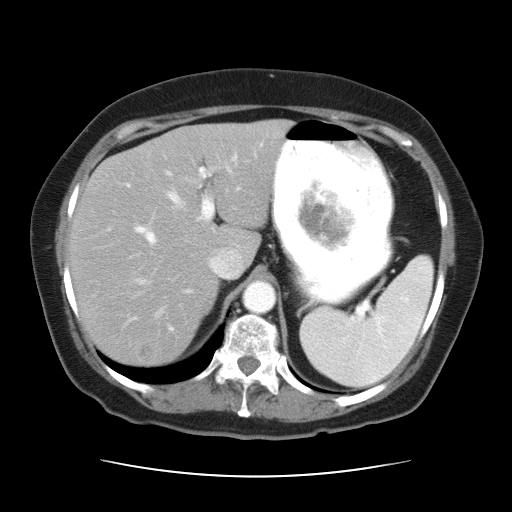
Contrast-enhanced abdominal CT, one axial slice. Position 23 of 34 along the scan axis. 120 kVp. Intravenous contrast given. Soft-tissue window (W 400 / L 40 HU). 7.5 mm slice thickness. 512 × 512 image matrix, field of view 360 × 360 mm. Female patient, age 65 years. From the clinical record (not read from this slice): diagnosis: colorectal cancer liver metastases, imaged before liver resection.
Structures marked on this image (expert manual segmentation):
- hepatic veins: bounding box (x1, y1, x2, y2) in pixels: (136, 171, 243, 295)
- liver: (72, 121, 289, 363)
- planned liver remnant (the part of the liver to remain after resection): (72, 121, 288, 350)
- portal vein (with intrahepatic branches): (125, 144, 262, 331)
- liver metastasis: (138, 343, 154, 359)